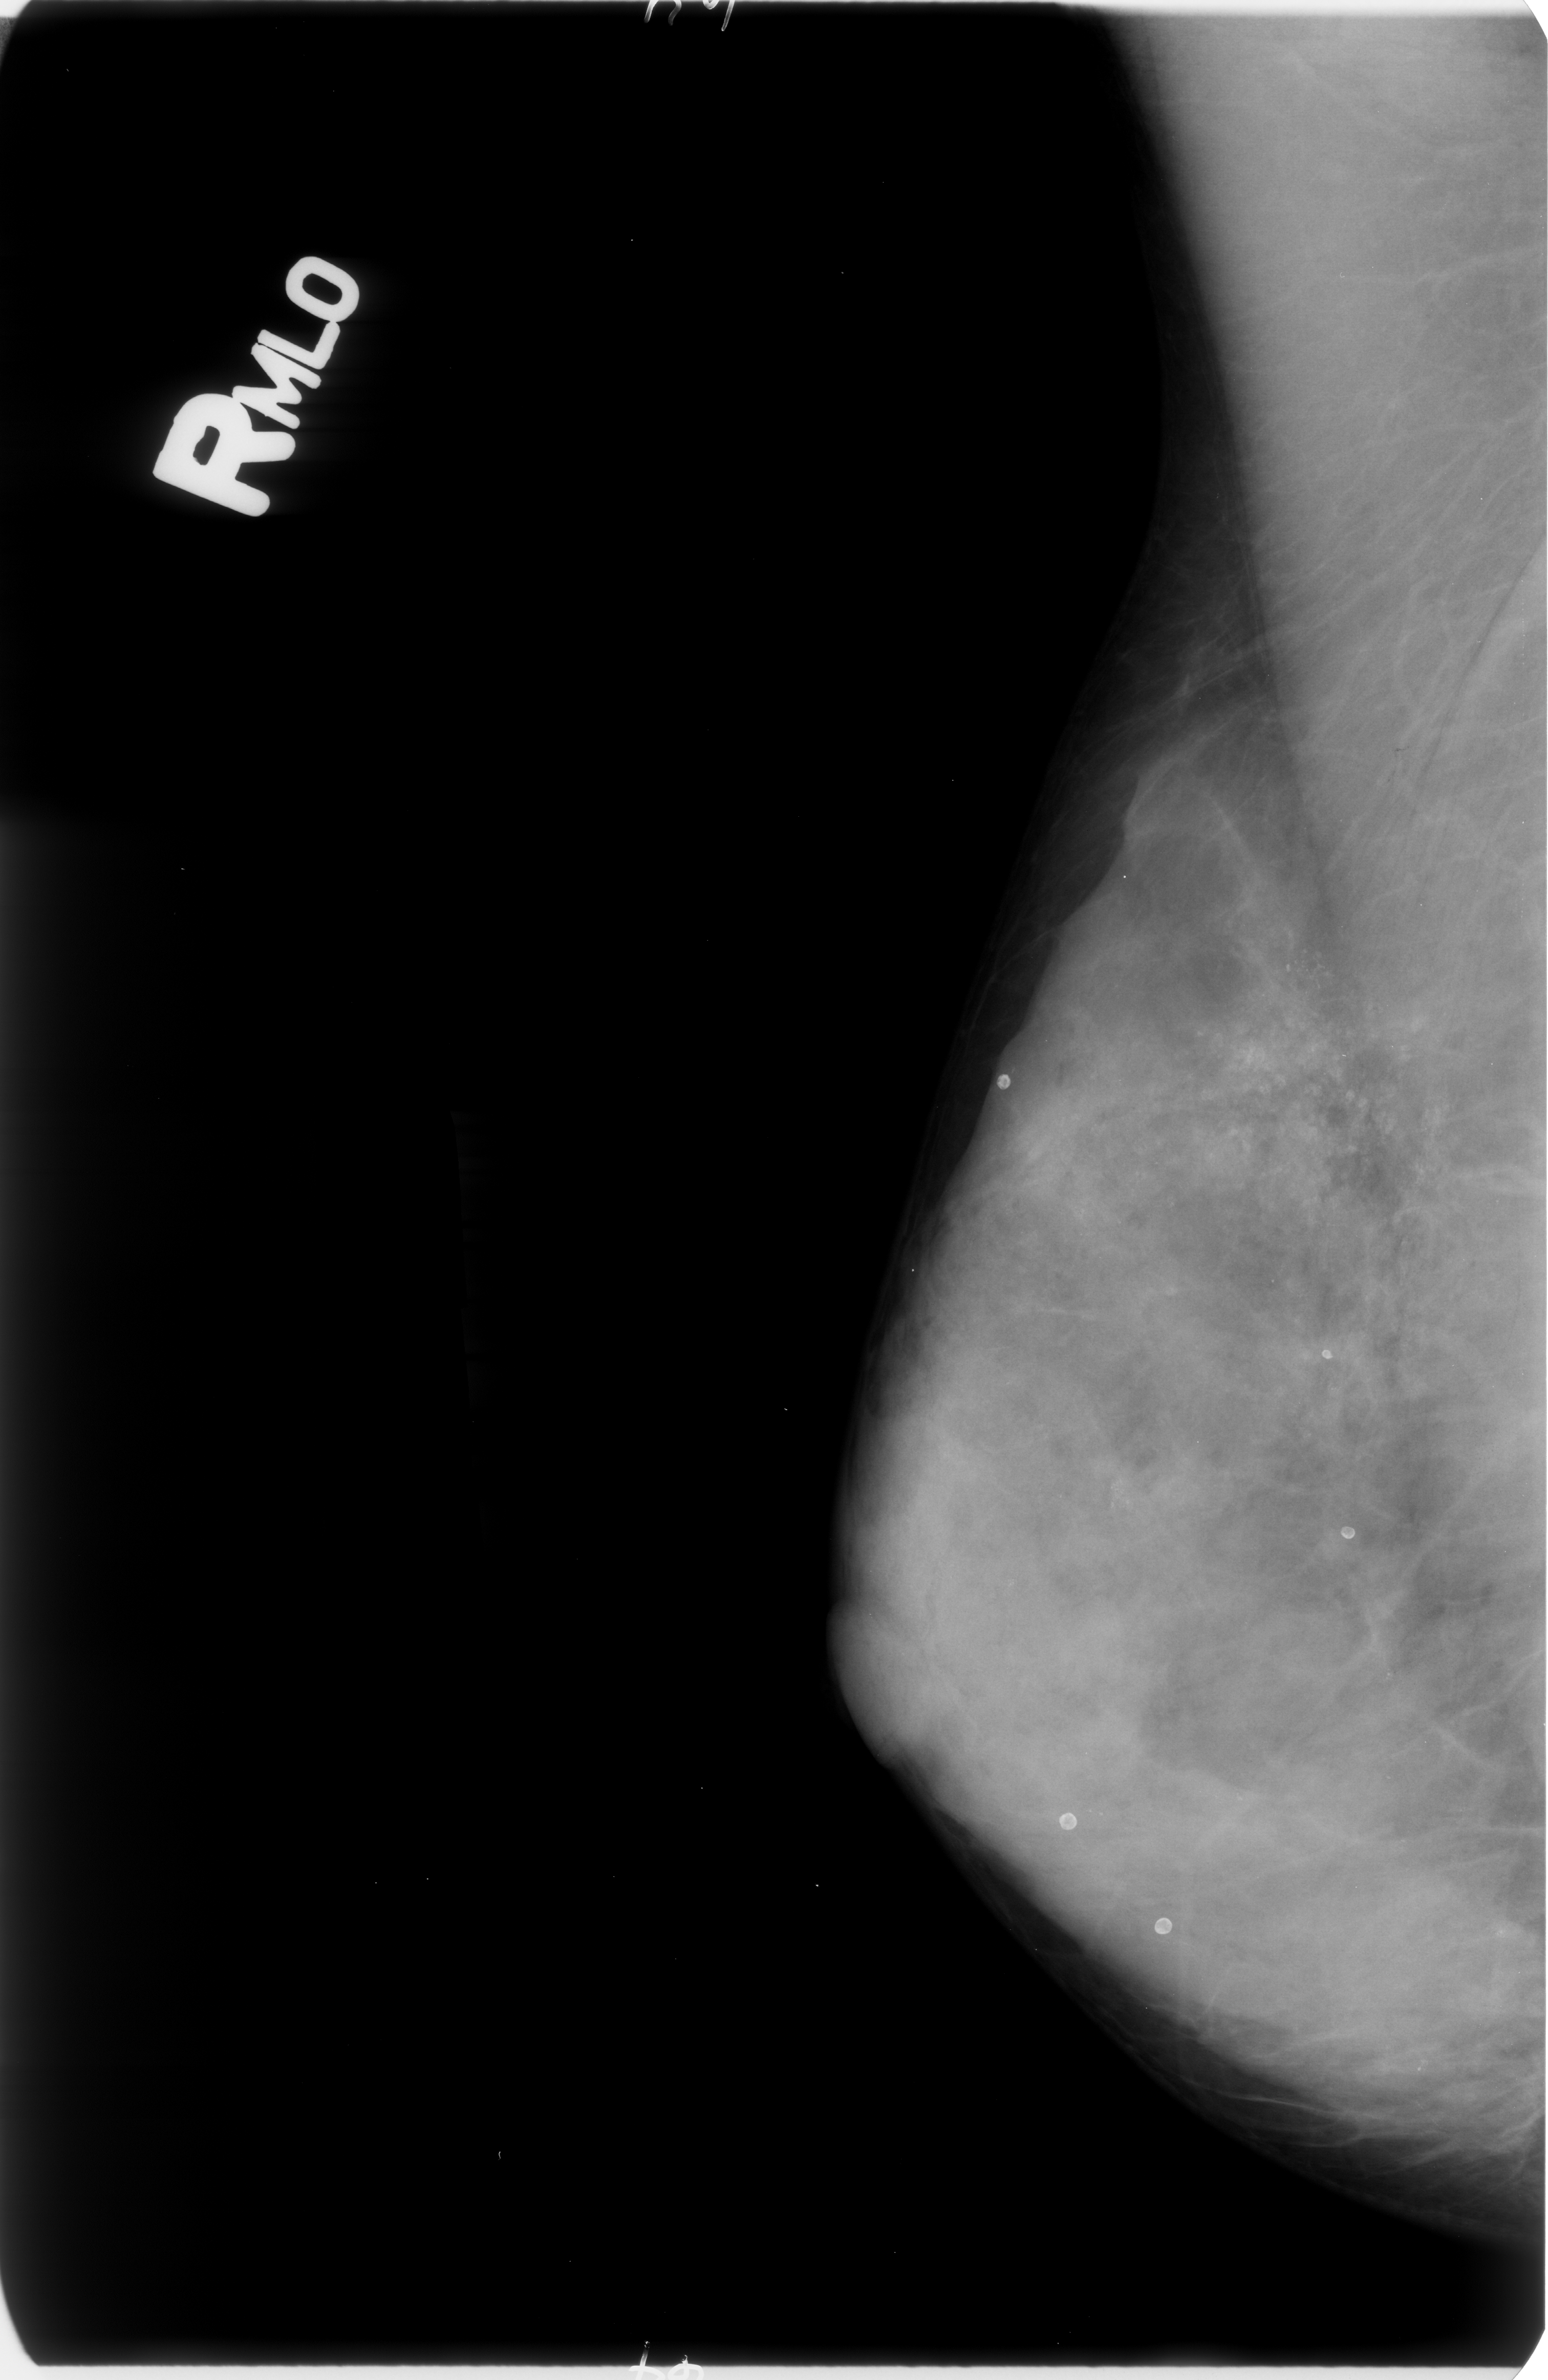
Scanned film-screen mammogram; right breast; MLO view; breast composition: extremely dense (BI-RADS density category 4 of 4); 1548 × 2380 image matrix.
Expert-marked regions of interest on this image (one box per marked abnormality):
- calcifications, morphology punctate / amorphous, distribution regional; BI-RADS assessment category 4; pathology (as recorded): benign: bounding box [x1, y1, x2, y2] px = [1023, 905, 1545, 1492]